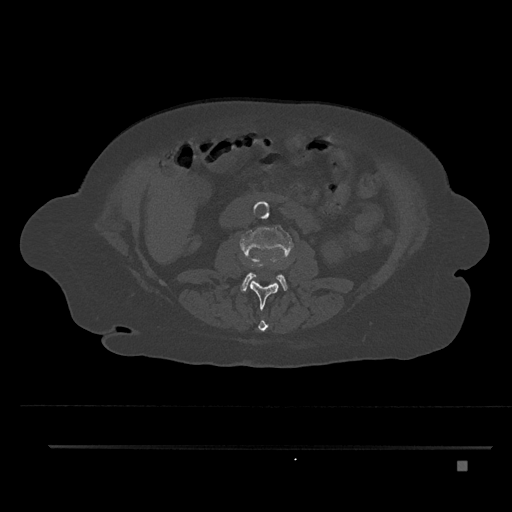
CT including the spine, one axial slice. 120 kVp. Bone window (W 1800 / L 400 HU). 0.5 mm slice thickness. 512 × 512 image matrix, field of view 437 × 437 mm. Patient: female, 76 years. From the clinical record (not read from this slice): primary cancer: lung; vertebrae with lytic lesions (as recorded): T11, L3.
Structures marked on this image (semi-automatic segmentation, software-assisted and operator-edited):
- L1 vertebra: bounding box (x1, y1, x2, y2) in pixels: (258, 320, 268, 332)
- L2 vertebra: (243, 263, 279, 310)
- L3 vertebra: (240, 225, 293, 292)